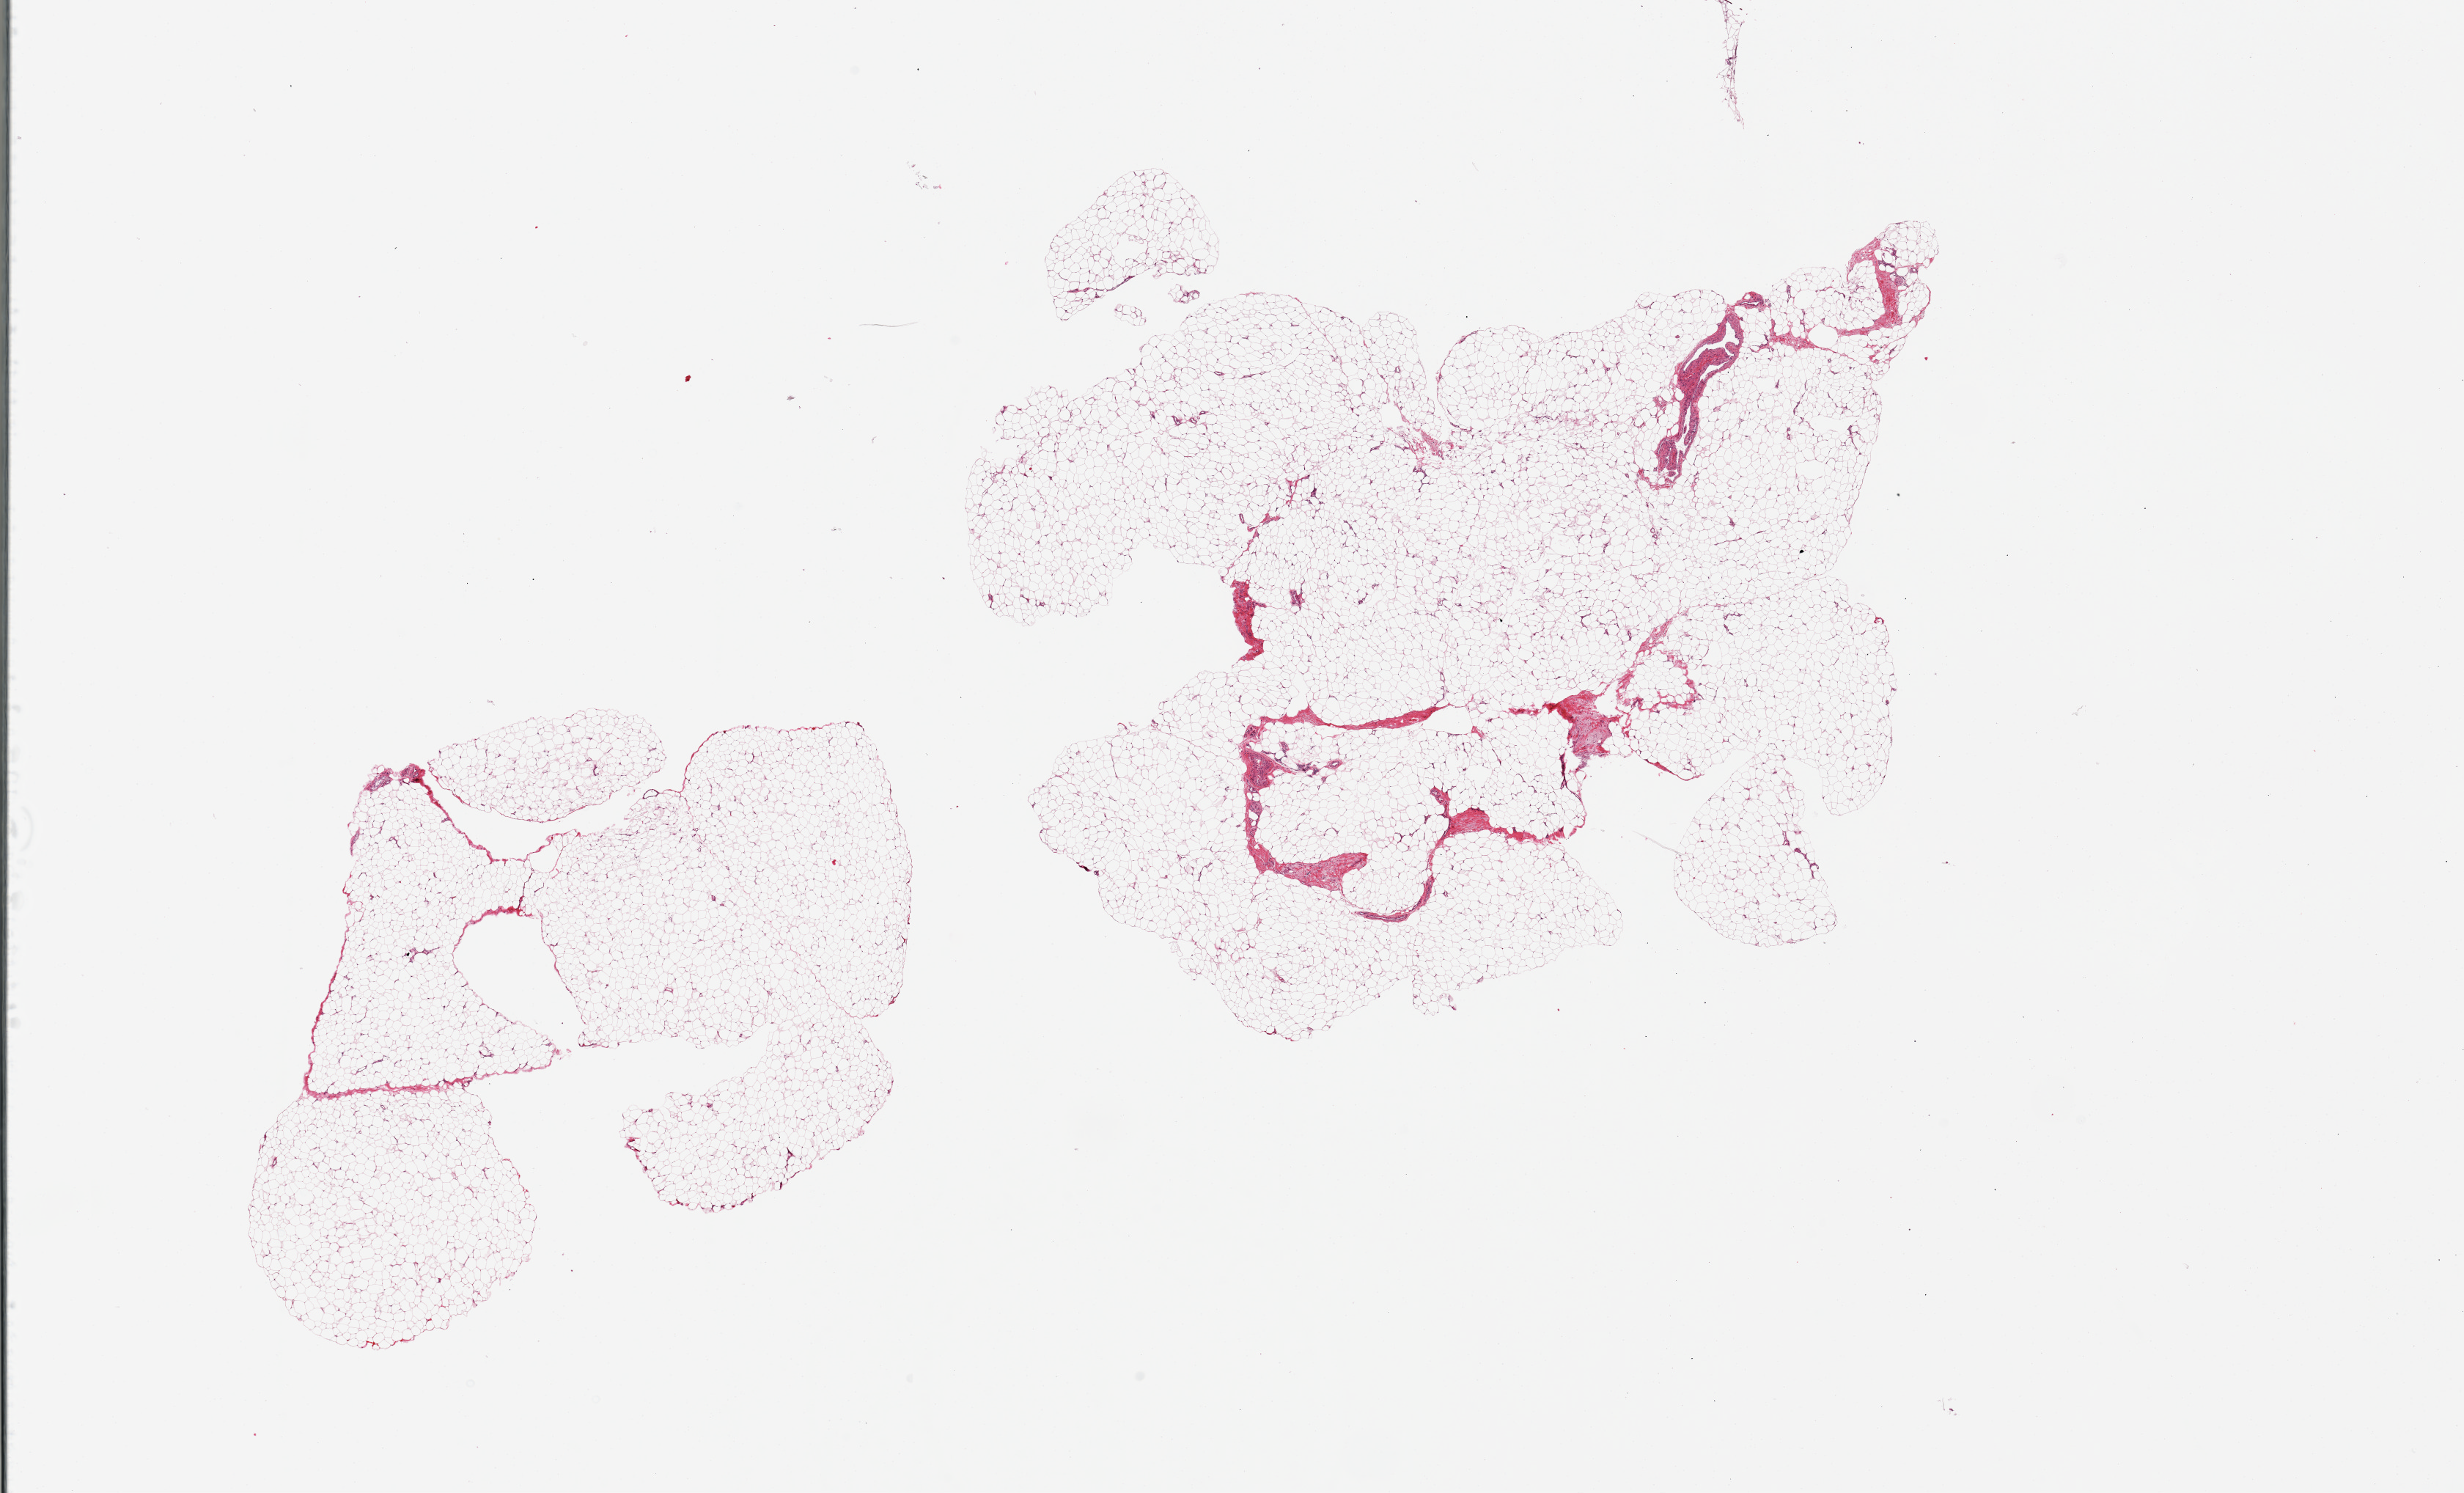
Whole-slide image, hematoxylin and eosin (H&E) stain, brightfield — shown as a low-resolution overview of the whole scanned area (about 26.6 x 16.1 mm); PAXgene-fixed paraffin-embedded (PFPE) section; section of adipose tissue (target tissue); tissue donor sample.
Pathologist's review note for this sample: 2 pieces, ~5-10% fibrous tissue/vessels.